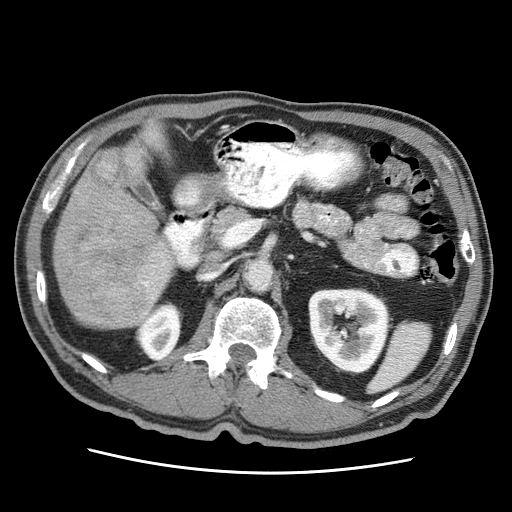
Contrast-enhanced abdominal CT (liver protocol), one axial slice; position 16 of 75 along the scan axis; reconstruction kernel STANDARD; 120 kVp; soft-tissue window (W 400 / L 40 HU); 512 × 512 image matrix. Case-level facts recorded for this patient, not image findings: diagnosis: hepatocellular carcinoma (patient treated with transarterial chemoembolisation; whether this scan precedes or follows treatment is not stated here); TNM stage (as recorded): Stage-IIIA; Child-Pugh class: A; tumour differentiation: well differentiated; tumour nodularity: multinodular.
Annotated regions visible in this slice (semi-automatic segmentation, software-assisted and operator-edited):
- liver parenchyma outside the tumour (the mass and vessels are separate outlines, so this box may not span the whole liver): bounding box <54,122,174,328> (left, top, right, bottom; pixels)
- mass: <54,150,156,324>
- liver vessels: <145,254,166,314>